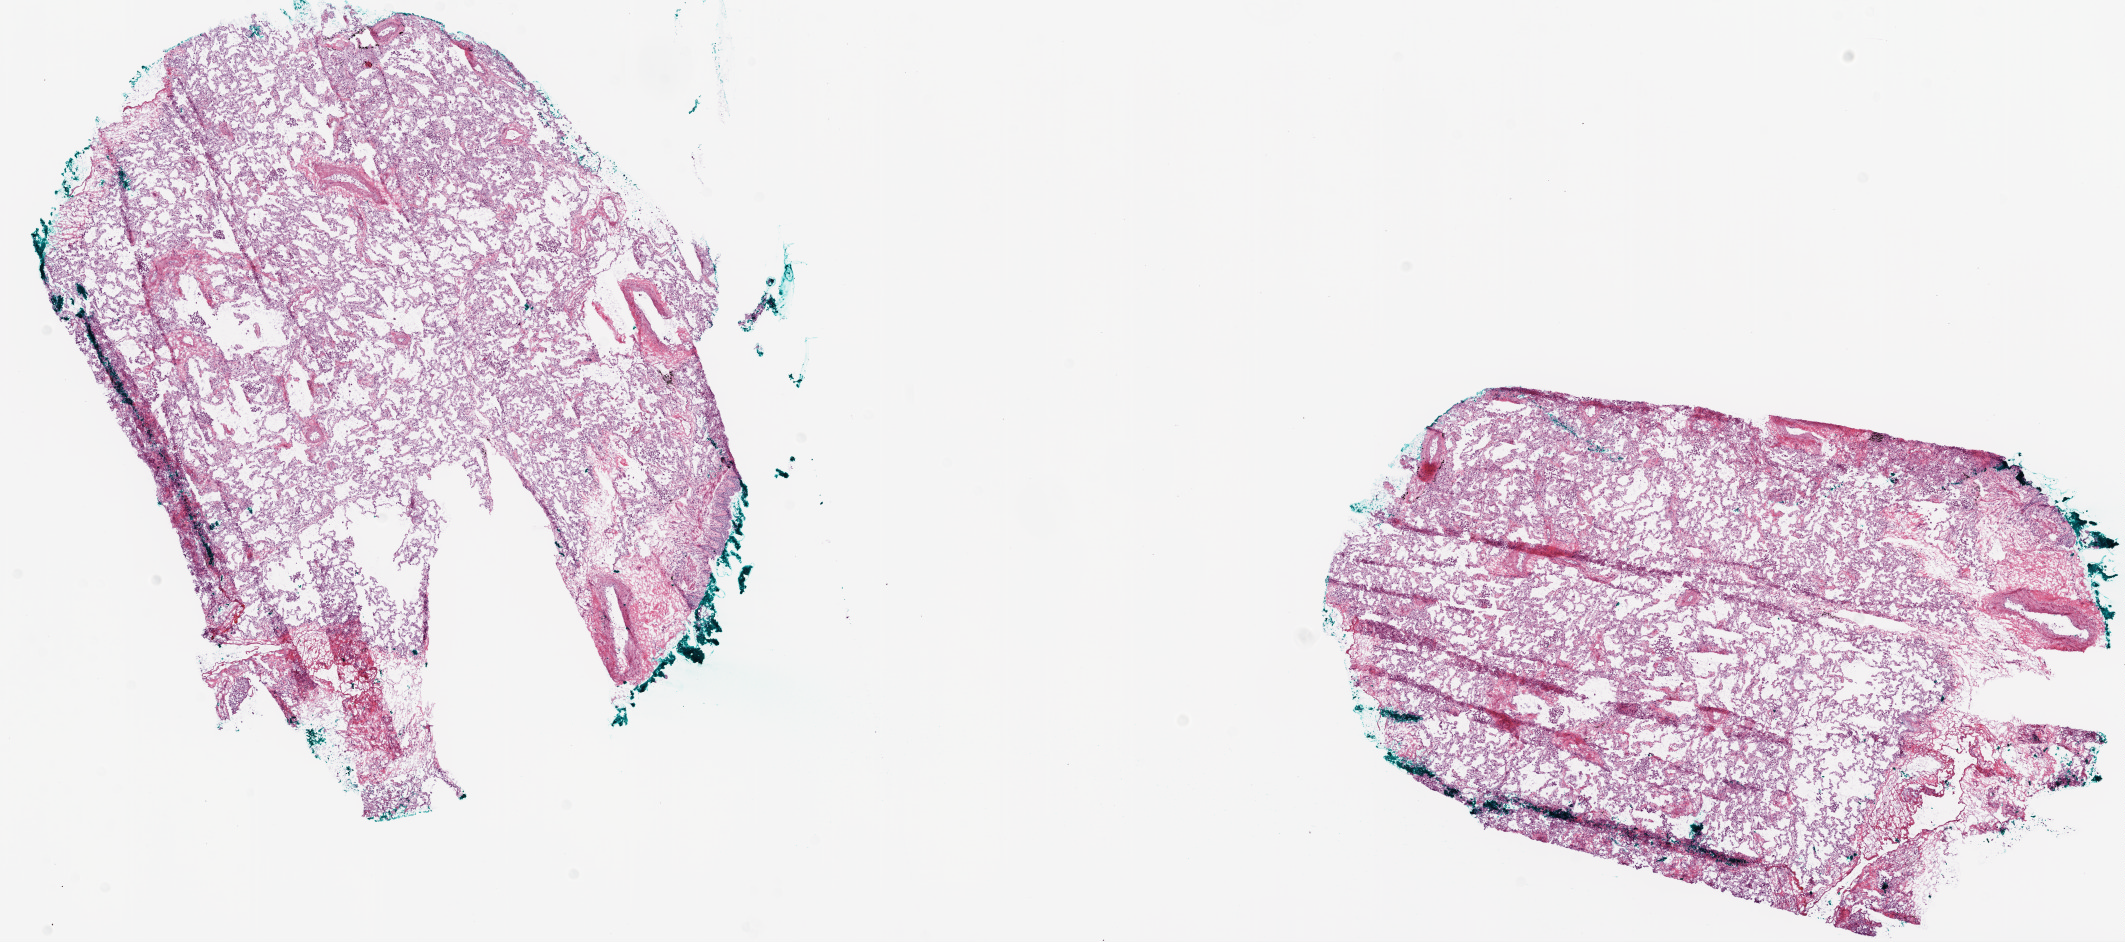
Digitized H&E tissue section (whole slide), a low-resolution overview of the entire scanned area, about 17.1 x 7.6 mm (acquisition: 20x scan), frozen section from the top of the tissue portion, lung, solid tissue normal (non-tumour tissue) sample. Male patient; age at initial diagnosis 58 years.
* this section: solid tissue normal sample (biorepository sample class)
* patient diagnosis: Squamous cell carcinoma, NOS (lower lobe, lung)